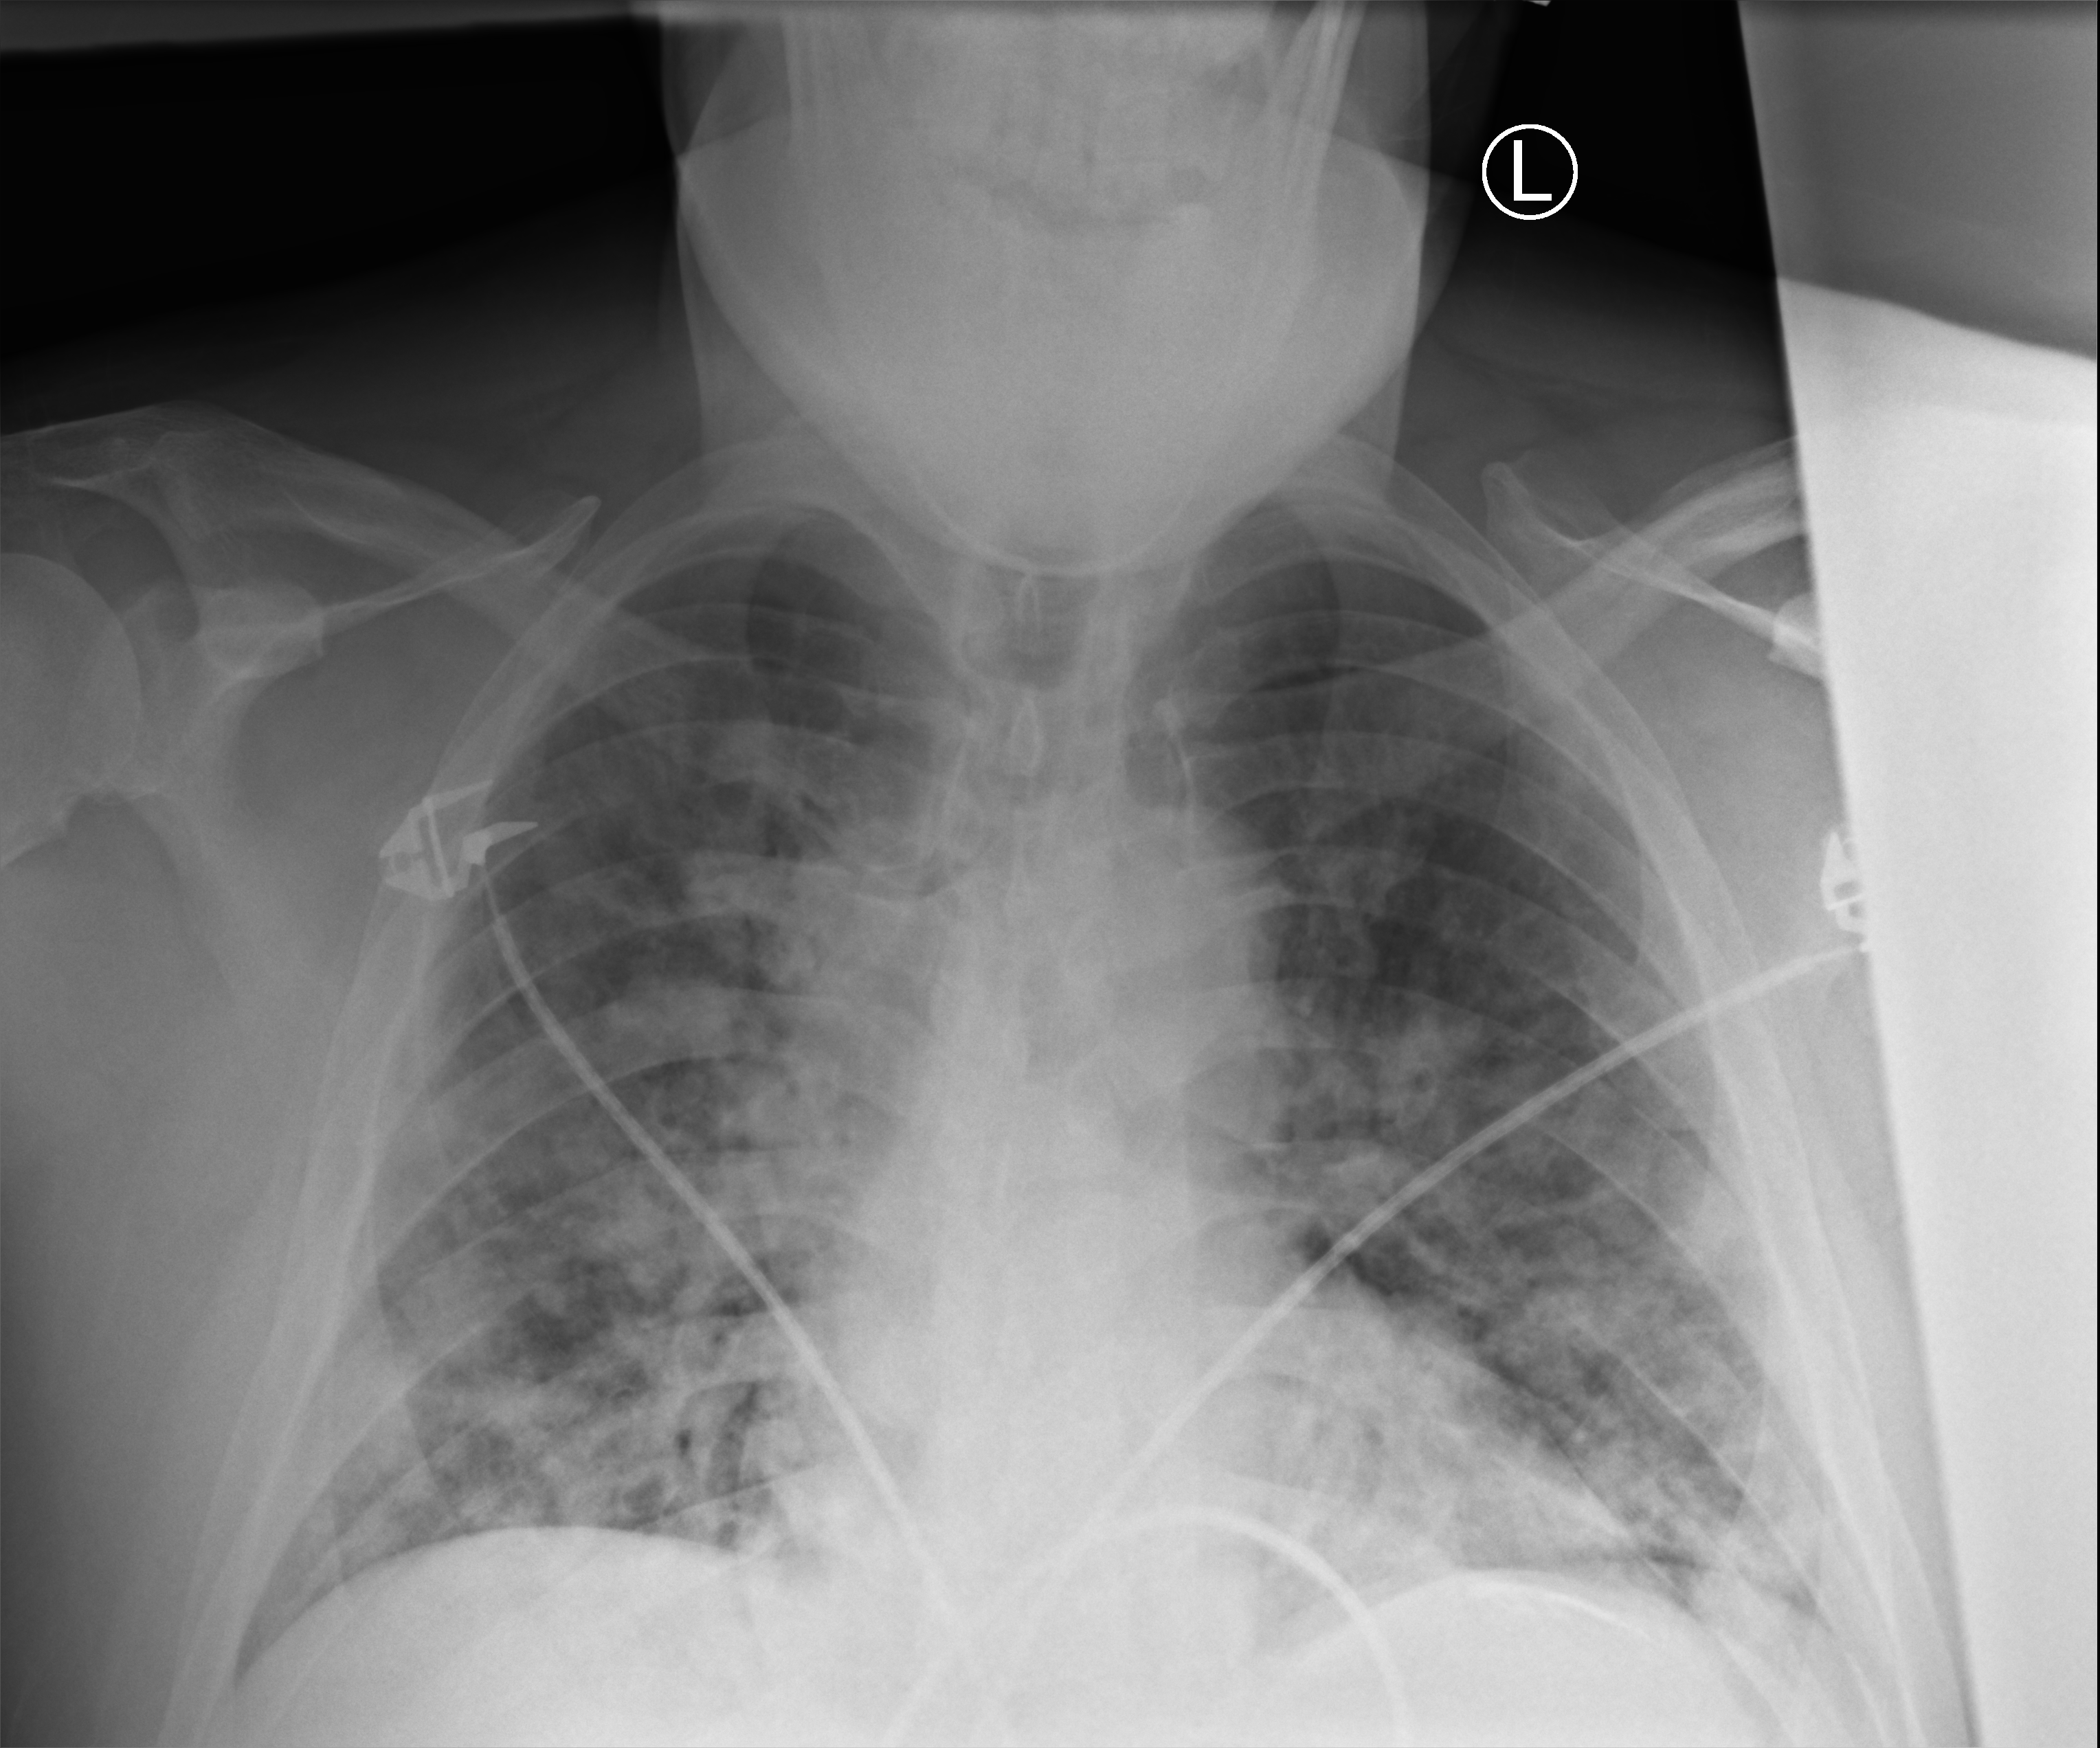
Bedside chest radiograph (computed radiography). Male patient hospitalised with COVID-19, age 18–59 years.
Hospital-stay facts (about this admission, not read from this image; timing relative to this image not recorded):
- admitted to intensive care during this hospital stay: no